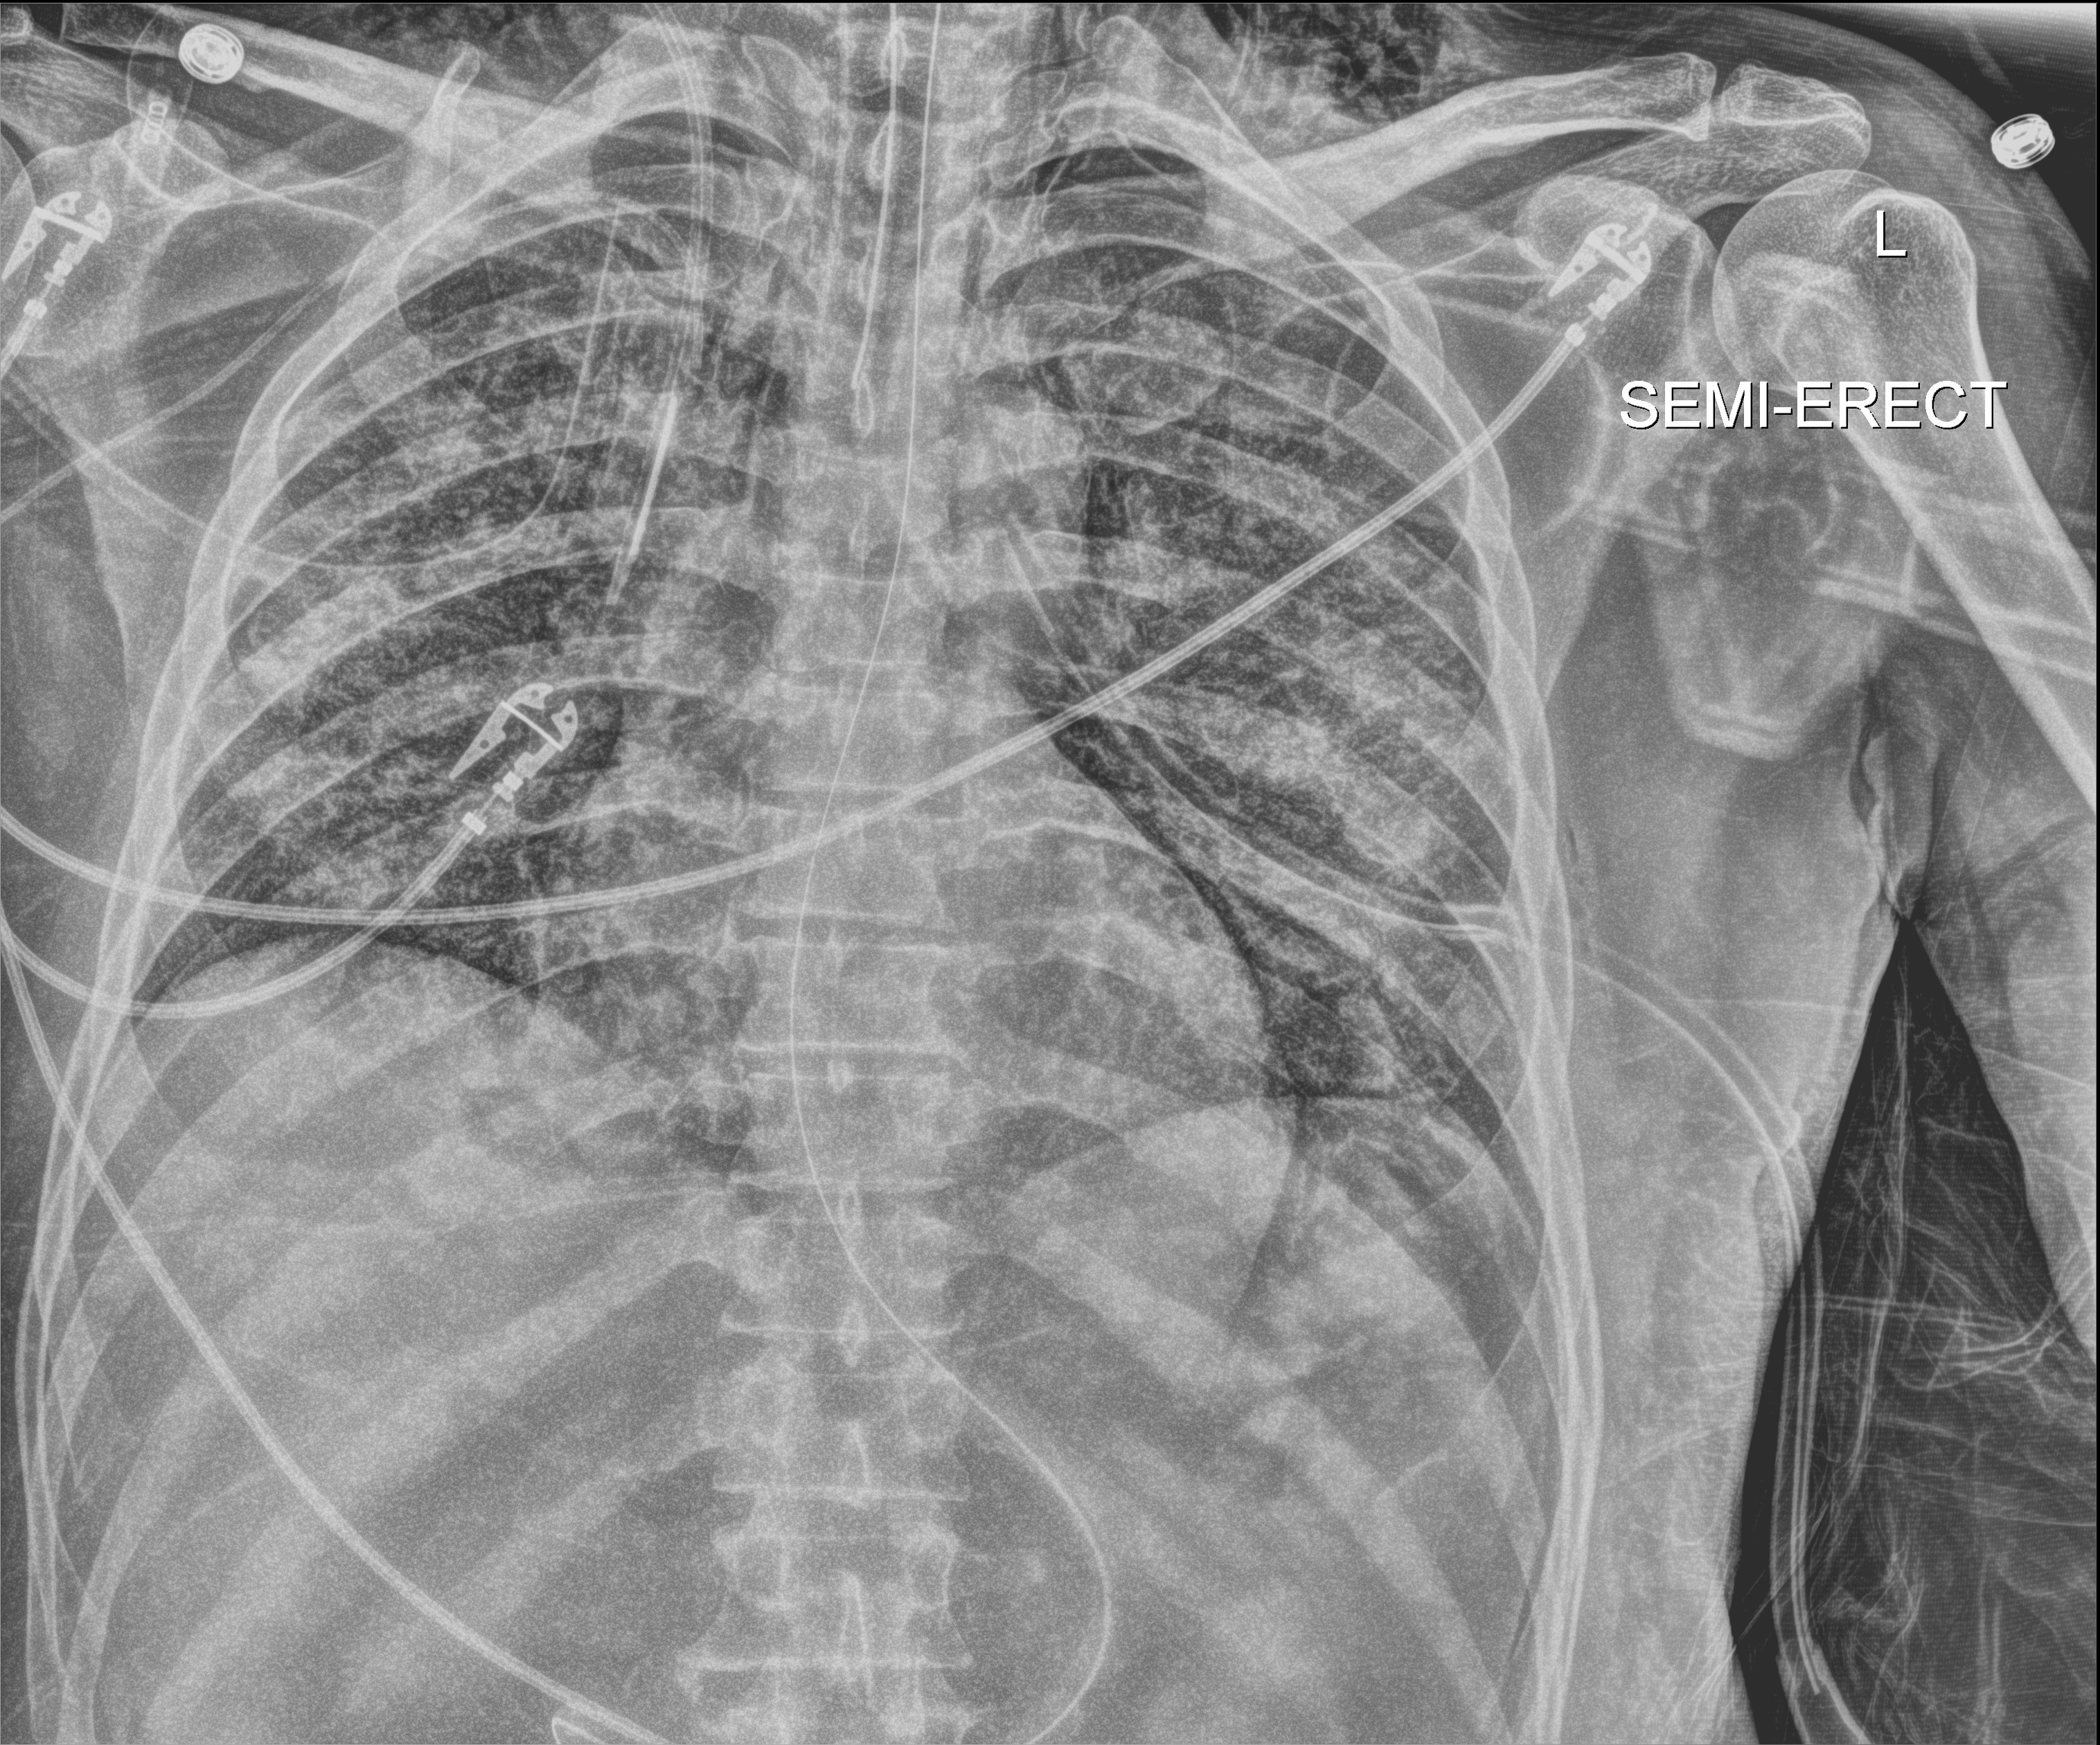
Chest X-ray (portable), anteroposterior (AP) projection. Male patient hospitalised with COVID-19, age 18–59 years.
Admission-level facts for this patient (not findings on this image; timing relative to this image not recorded):
- length of hospital stay: 77 days